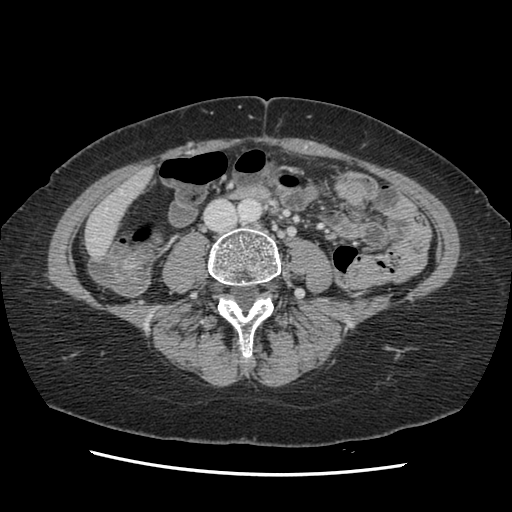
Contrast-enhanced abdominal CT, one axial slice. Position 19 of 141 along the scan axis. Soft-tissue window (W 400 / L 40 HU). 512 × 512 image matrix. Female patient, age 61 years. From the clinical record (not read from this slice): diagnosis: colorectal cancer liver metastases, imaged before liver resection; multiple liver metastases: no; largest metastasis: 2.4 cm; disease in both lobes: no.
Structures marked on this image (outlined manually by an expert reader):
- hepatic veins: box from (x=95, y=208) to (x=107, y=238) px
- liver: (x=86, y=170)–(x=151, y=256)
- planned liver remnant (the part of the liver to remain after resection): (x=86, y=170)–(x=151, y=256)